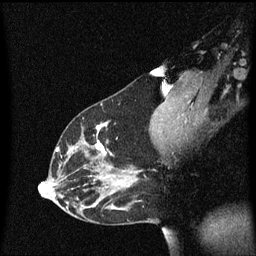
Breast MRI (dynamic contrast-enhanced), one sagittal slice. Slice 35 of 60 in the series (ordered by position). Dynamic contrast-enhanced series, image 2 of 3 at this slice position (ordered by acquisition). 1.5 T. TE 4.2 ms, TR 8.4 ms. 2 mm slice thickness. 256 × 256 image matrix, field of view 200 × 200 mm. Patient: female, 33 years.
Annotated regions visible in this slice (semi-automatically segmented with operator editing):
- analysis volume of interest (the breast-tissue region the enhancement analysis was run in; not a lesion): bounding box [x1, y1, x2, y2] px = [45, 116, 152, 191]
- tumour enhancement mask (voxels above the 70 % enhancement threshold inside the analysis volume of interest): [57, 122, 109, 179]